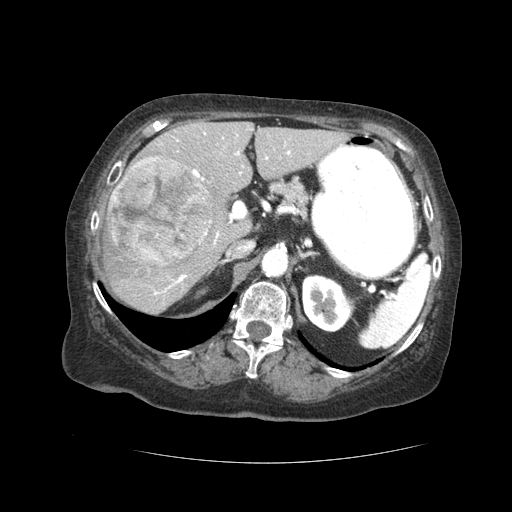
Contrast-enhanced abdominal CT (liver protocol), one axial slice; slice 23 of 59 in the series (ordered by position); reconstruction kernel STANDARD; soft-tissue window (W 400 / L 40 HU); 512 × 512 image matrix, field of view 380 × 380 mm. Case-level facts recorded for this patient, not image findings: diagnosis: hepatocellular carcinoma (patient treated with transarterial chemoembolisation; whether this scan precedes or follows treatment is not stated here); TNM stage (as recorded): Stage-I; Child-Pugh class: A; tumour nodularity: uninodular.
Annotated regions visible in this slice (semi-automatically segmented with operator editing):
- liver parenchyma outside the tumour (the mass and vessels are separate outlines, so this box may not span the whole liver): box from (x=104, y=120) to (x=346, y=312) px
- mass: (x=107, y=157)–(x=212, y=267)
- liver vessels: (x=154, y=132)–(x=291, y=295)